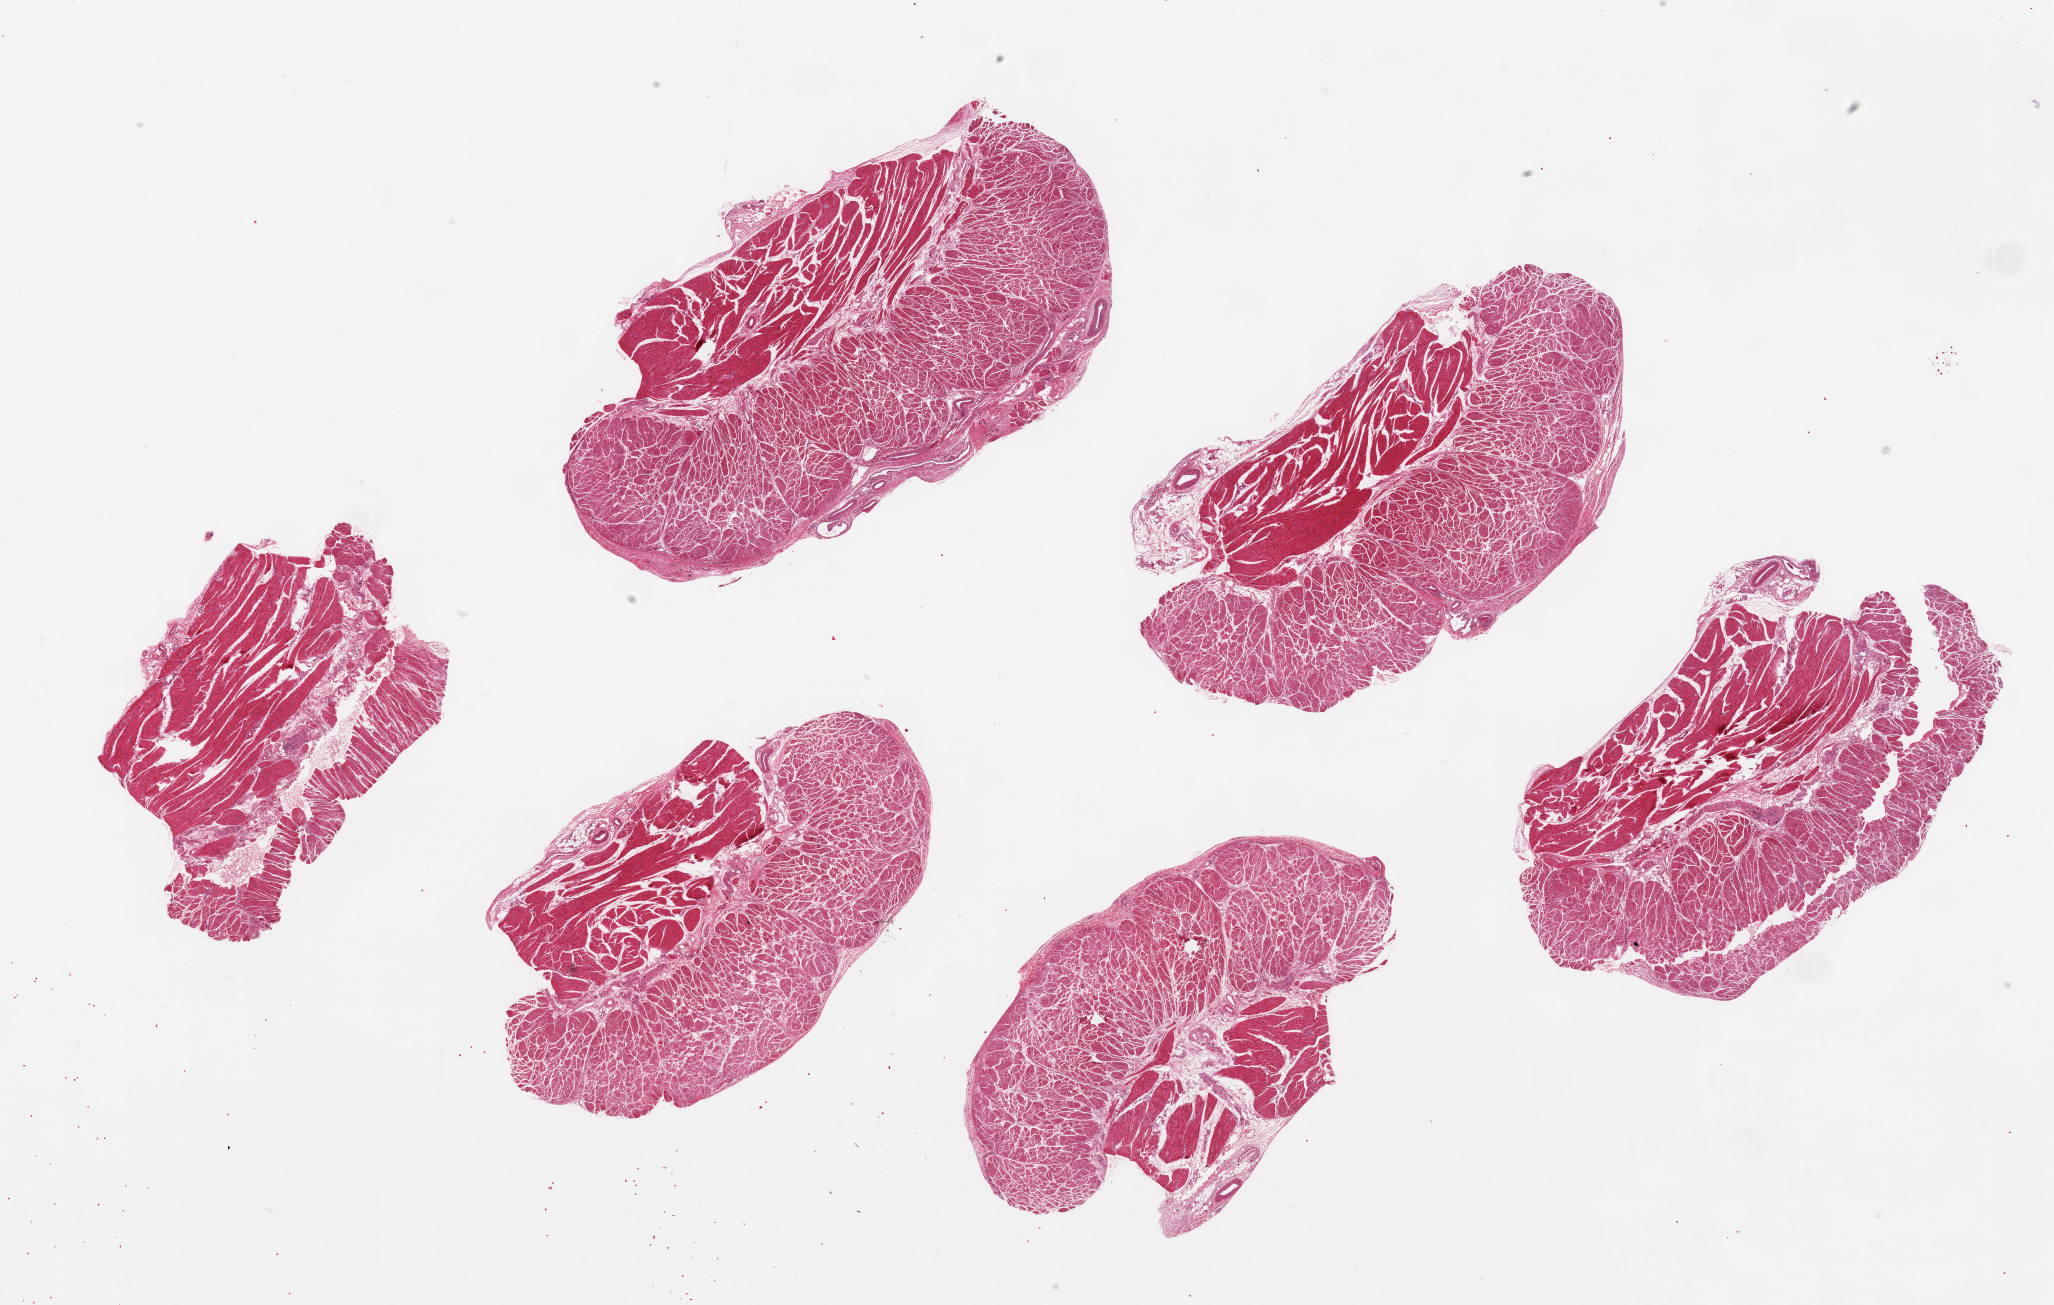
Digitized hematoxylin and eosin (H&E)-stained section, brightfield — a low-resolution overview of the entire scanned area, about 32.5 x 20.6 mm (slide scanned at 20x). PAXgene-fixed paraffin-embedded (PFPE) section. Section of esophageal muscle (target tissue). Tissue donor sample. Male donor.
Reviewer comment on this tissue sample: 6 pieces, ~8x5mm.